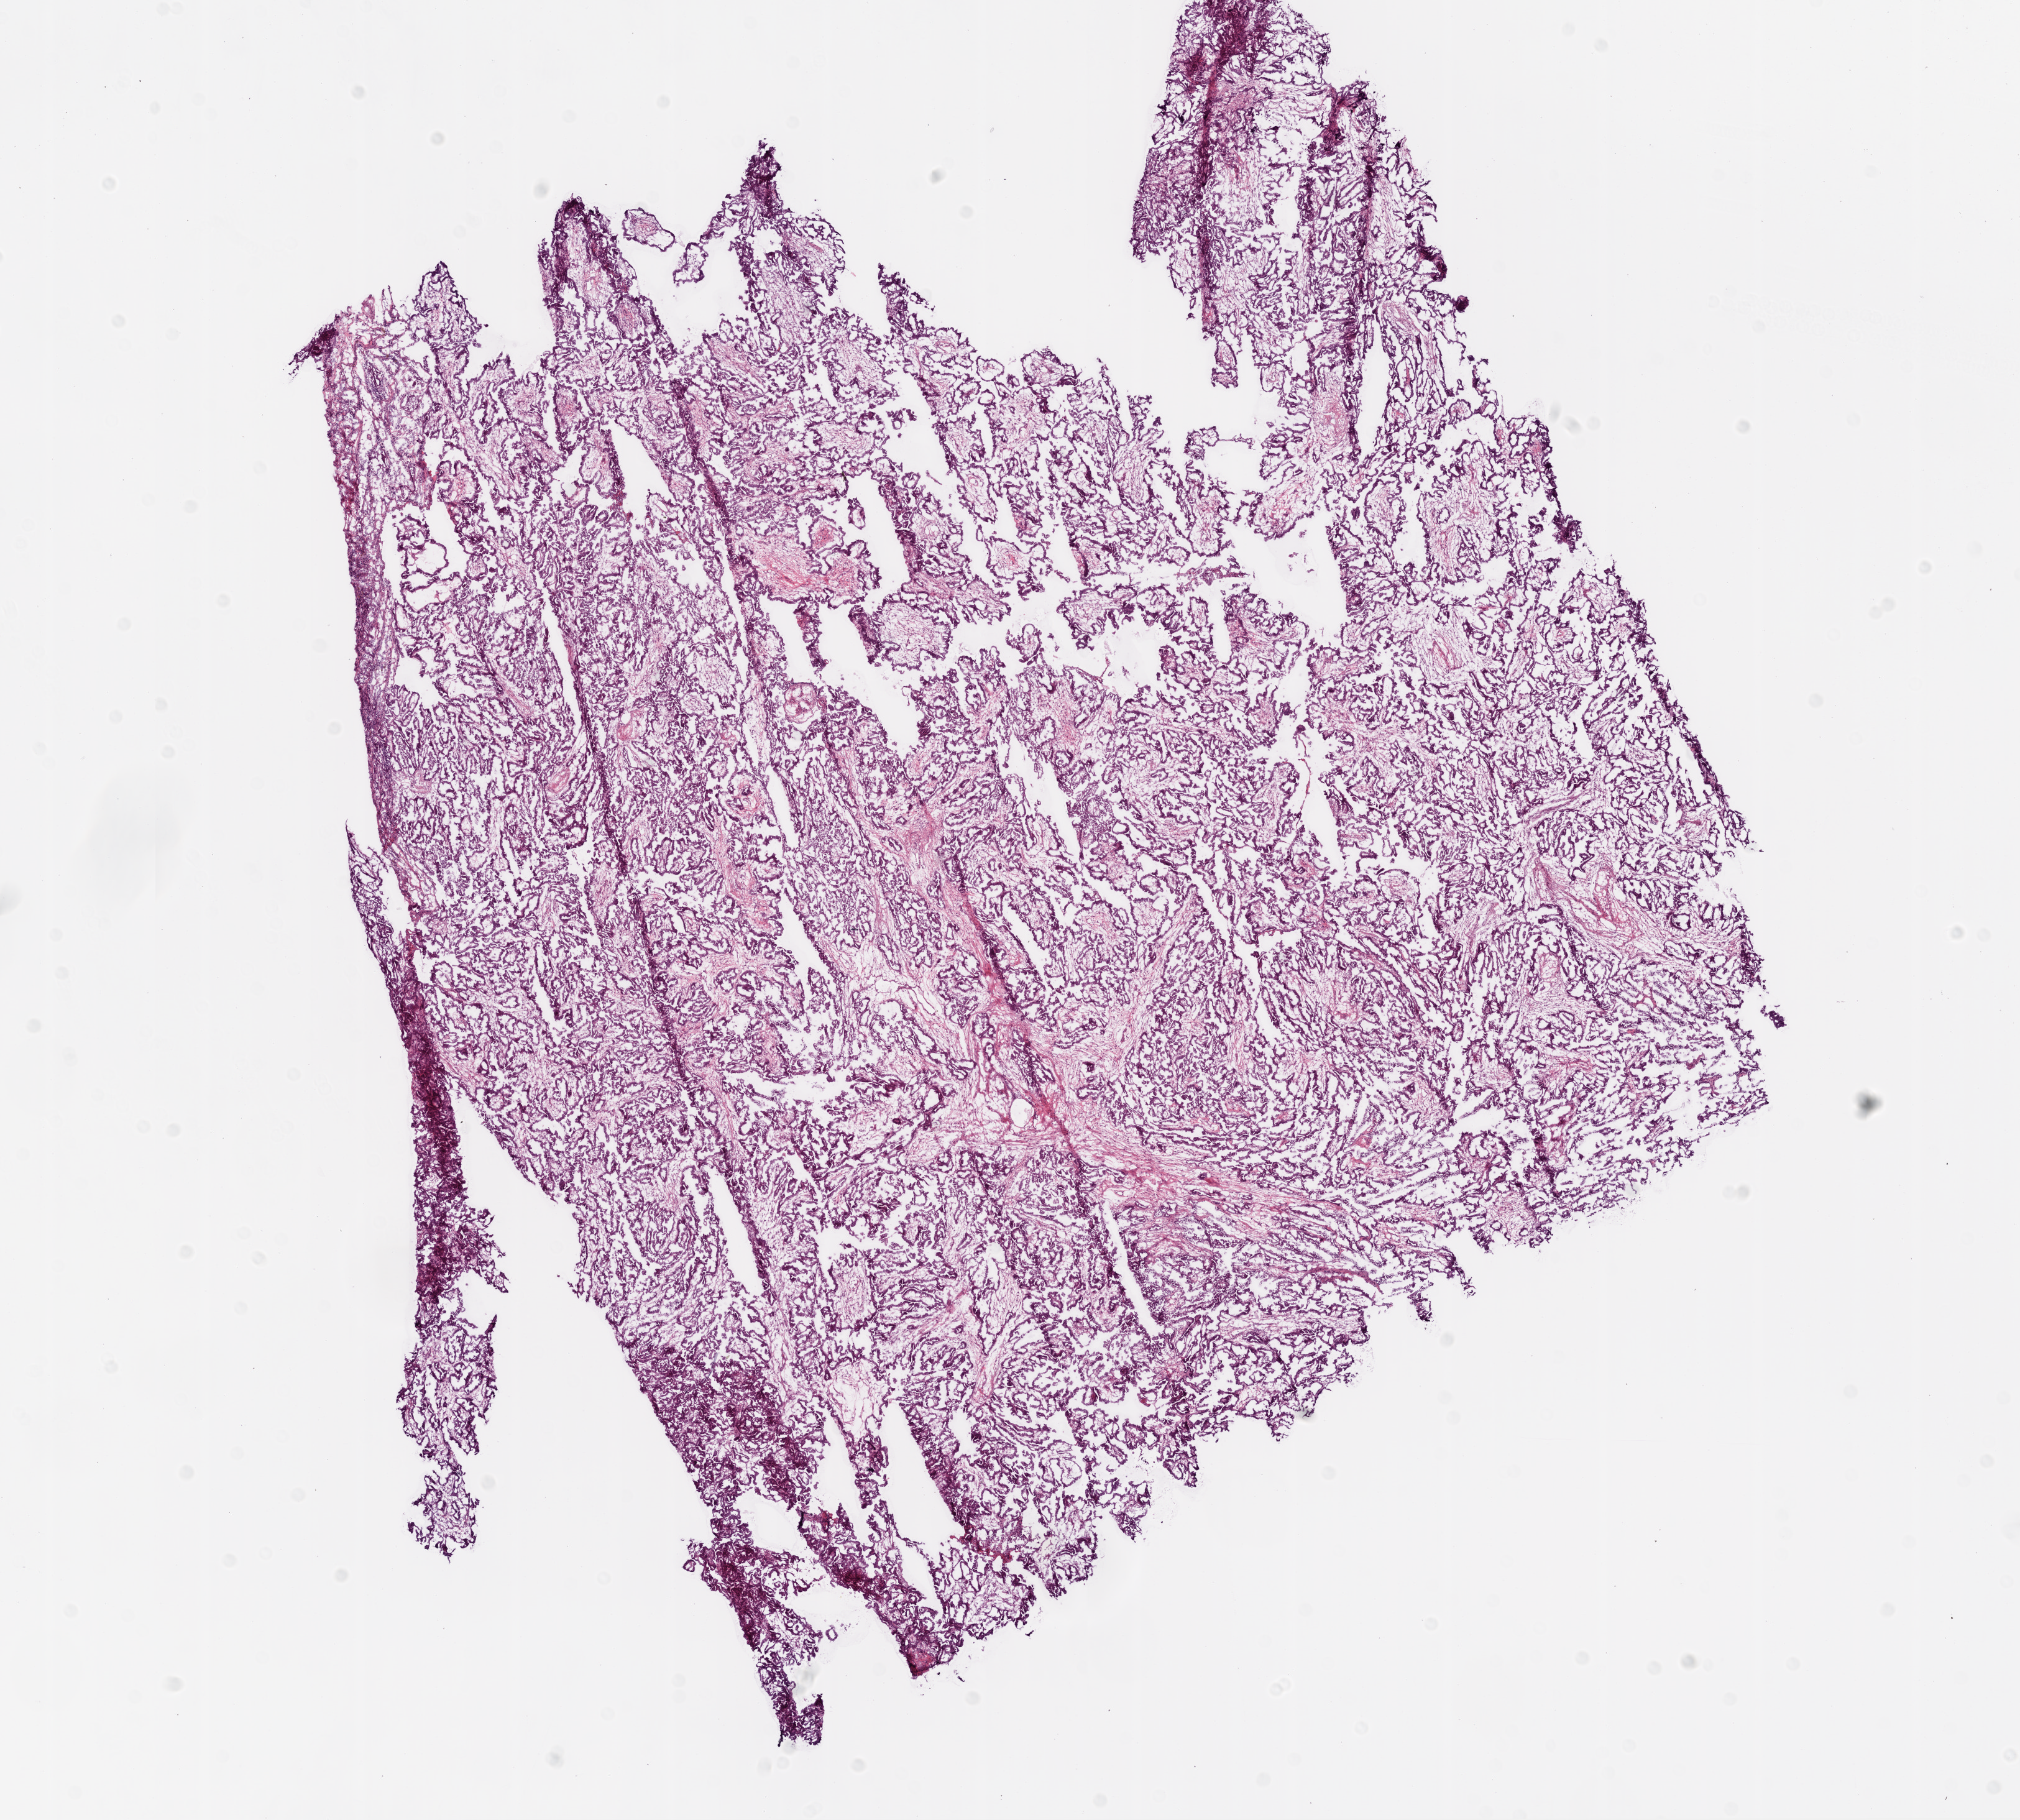
Digitized H&E tissue section (whole slide) — a low-resolution overview of the entire scanned area, about 13.0 x 11.7 mm (slide scanned at 20x); frozen section from the bottom of the tissue portion; sample: primary tumour, ovary. Female, age 72 years at initial diagnosis. Composition of this section per pathologist review: tumour cells 95%, tumour nuclei 80%.
Pathologic diagnosis: Serous cystadenocarcinoma, NOS.